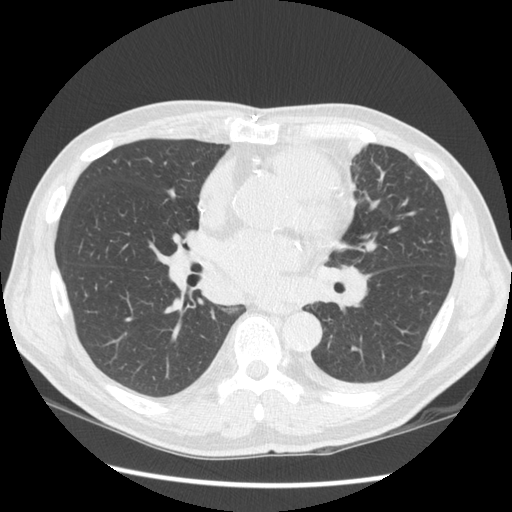
Low-dose screening chest CT, one axial slice; reconstruction kernel STANDARD; lung window (W 1500 / L -600 HU); 2.5 mm slice thickness; 512 × 512 image matrix.
Outlined on this slice (outlined manually by an expert reader):
- lesion 1 (tumor, upper lobe of left lung): bounding box (x1, y1, x2, y2) in pixels: (331, 139, 366, 167)